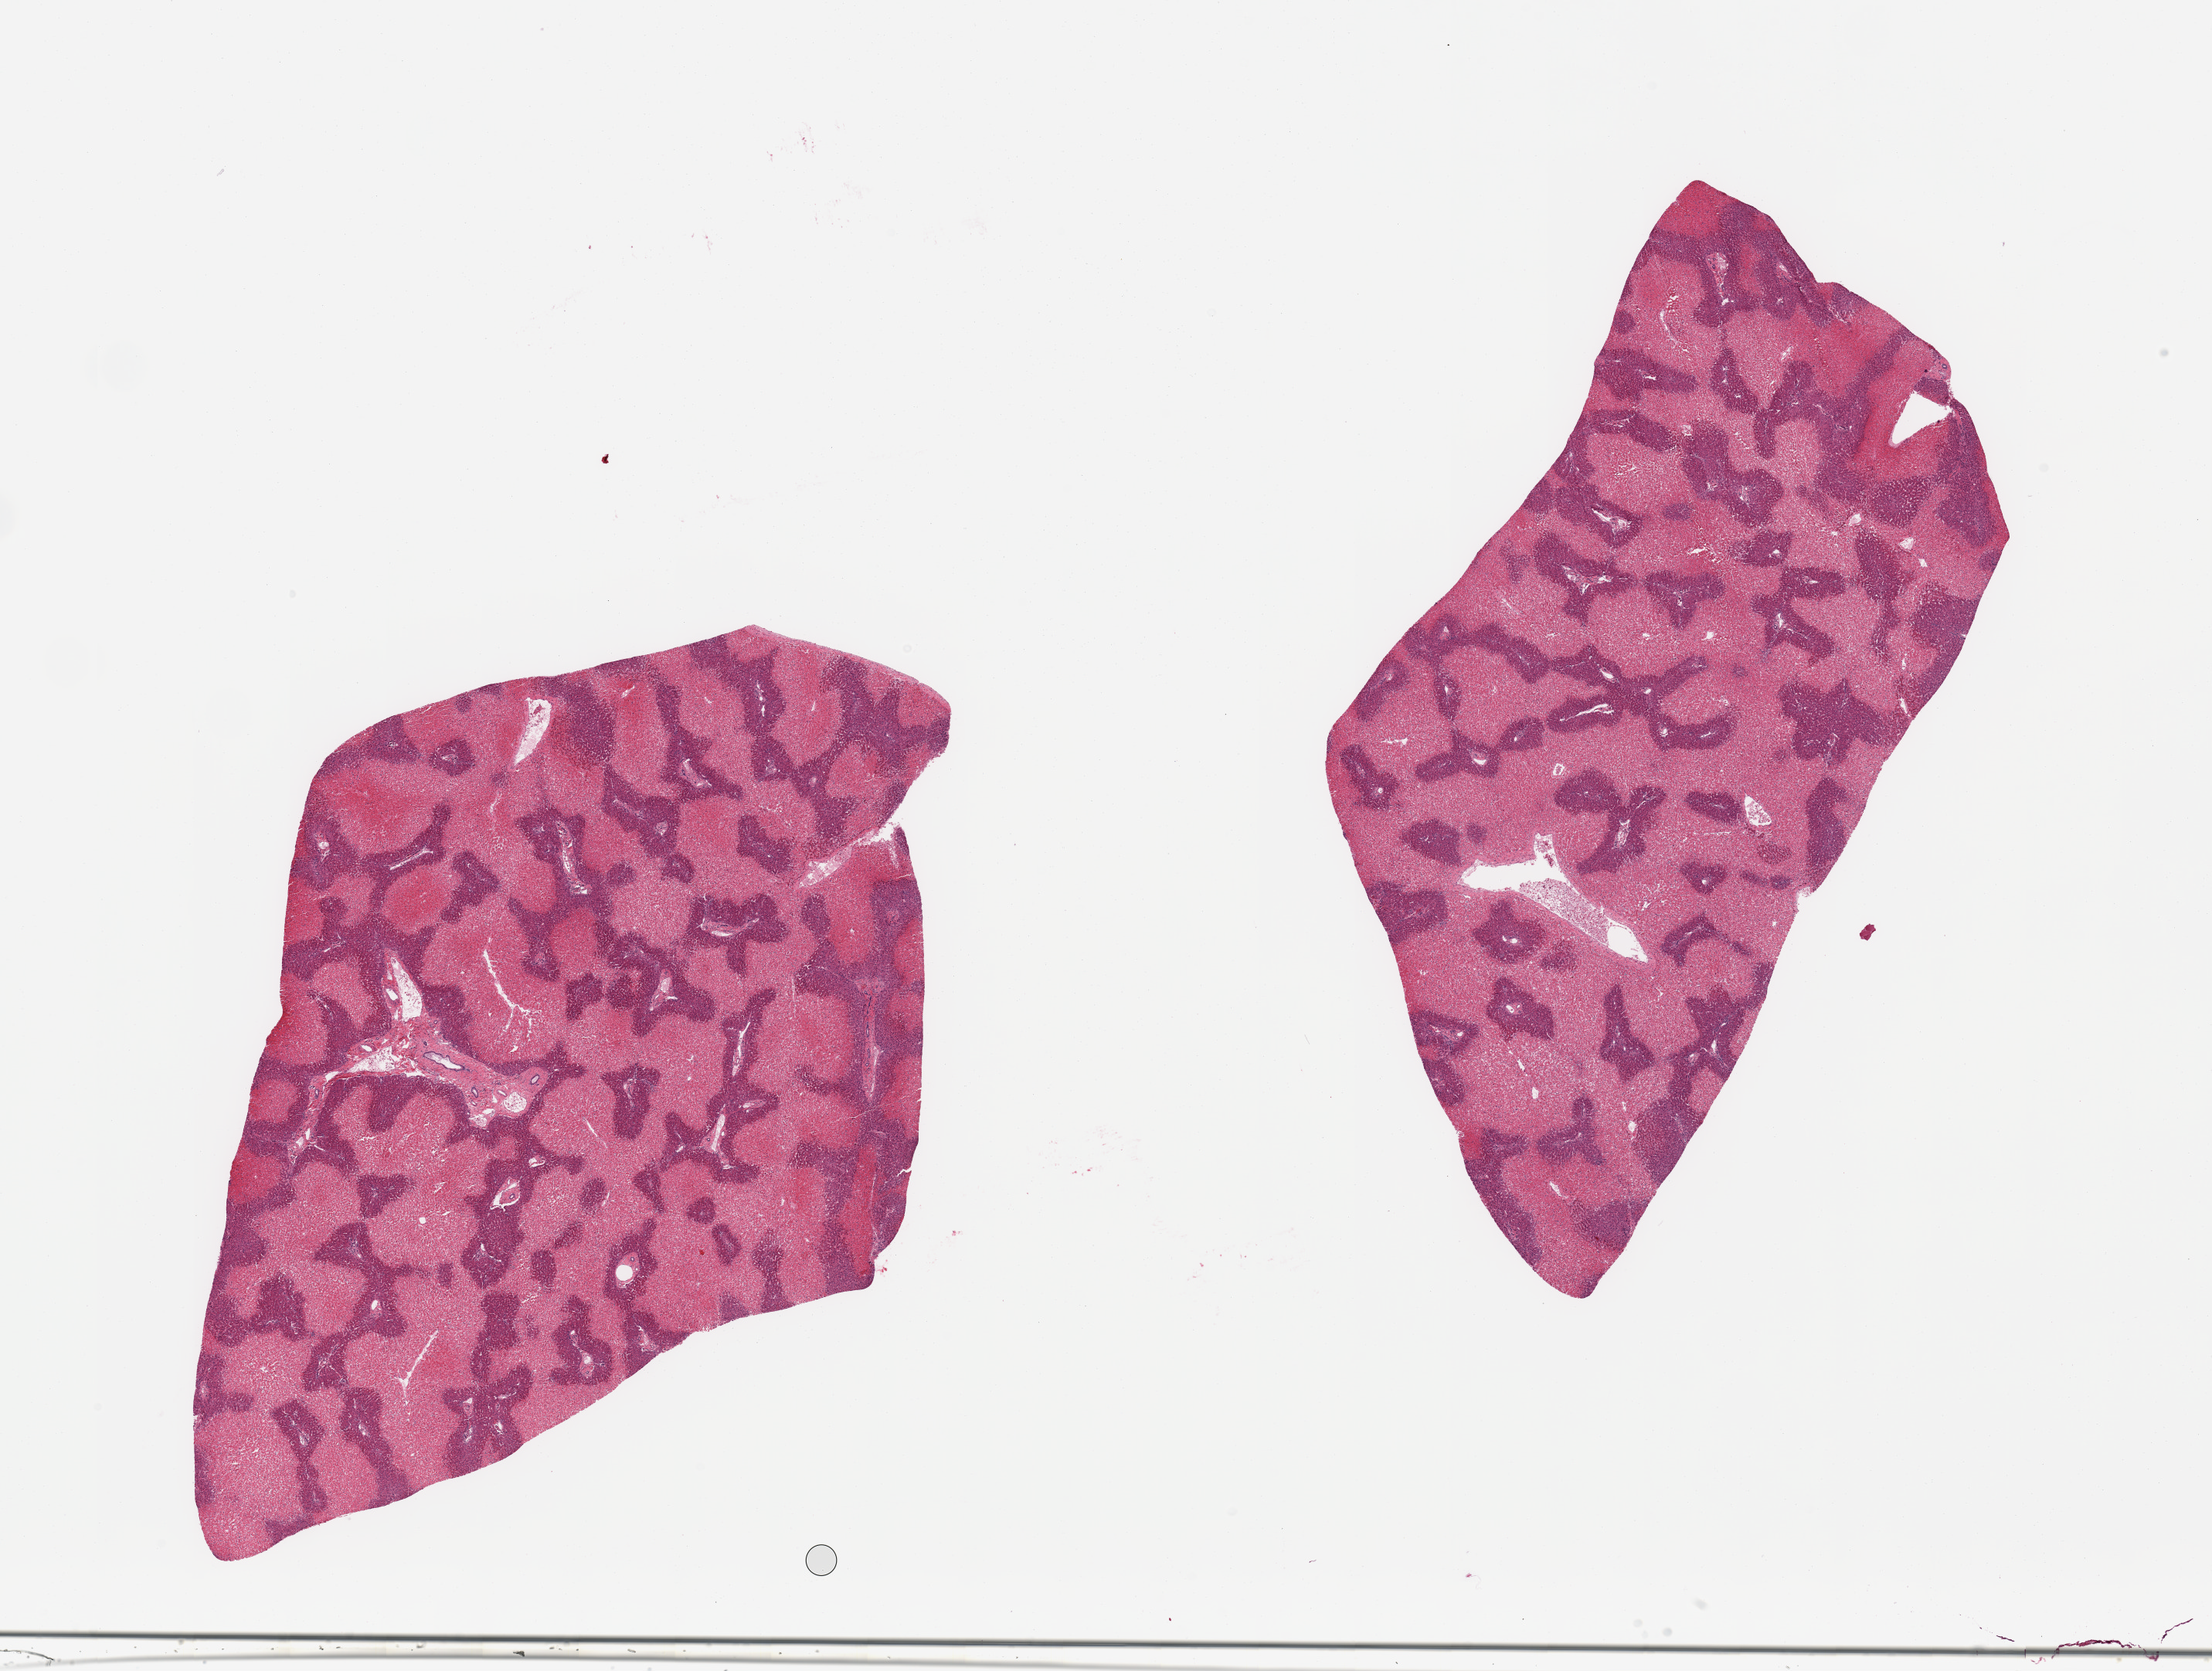
Digitized haematoxylin and eosin-stained section — whole scanned area (about 22.6 x 17.1 mm, acquisition: 20x scan) shown as a low-resolution overview, PAXgene-fixed paraffin-embedded (PFPE) section, section of liver (target tissue), donor tissue sample. Donor sex: female.
- reviewer comment on this tissue sample: 2 pieces; extensive central necrosis consistent with chemical/medication injury or prolonged hypotension